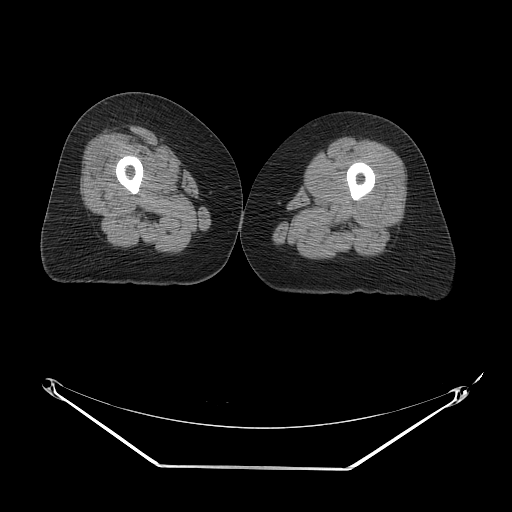
CT of an extremity soft-tissue mass (from a PET/CT study), one axial slice; slice 13 of 267 in the series (ordered by position); reconstruction kernel STANDARD; 140 kVp; soft-tissue window (W 400 / L 40 HU); 3.75 mm slice thickness; 512 × 512 image matrix, field of view 500 × 500 mm. Female patient. From the clinical record (not read from this slice): histological type: malignant solitary fibrous tumor; grade: intermediate; site of the primary tumour: right thigh.
Structures marked on this image (expert contour drawn on MRI and transferred to this co-registered scan by the dataset authors):
- gross tumour volume including surrounding oedema: bounding box [x1, y1, x2, y2] px = [130, 130, 181, 163]